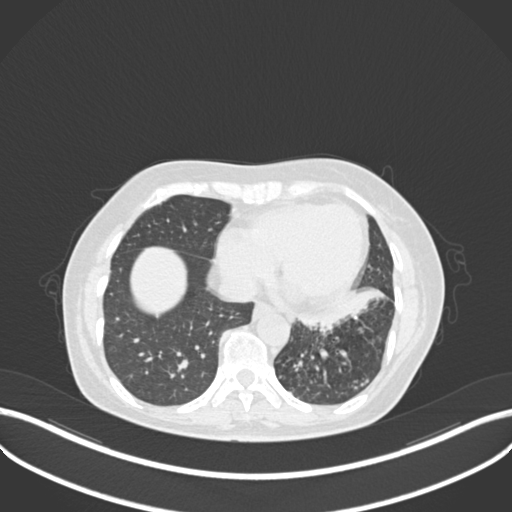
Chest CT, one axial slice. Position 83 of 270 along the scan axis. Reconstruction kernel B30f. Lung window (W 1500 / L -600 HU). 512 × 512 image matrix, field of view 400 × 400 mm. Patient: female, 63 years. From the clinical record (not read from this slice): clinical TNM (as recorded): T1b N0 M0; histopathological grade: G2-3.
Outlined on this slice (rectangle marked by the reading radiologist):
- lung tumour (recorded histology: adenocarcinoma): box from (x=292, y=287) to (x=387, y=330) px